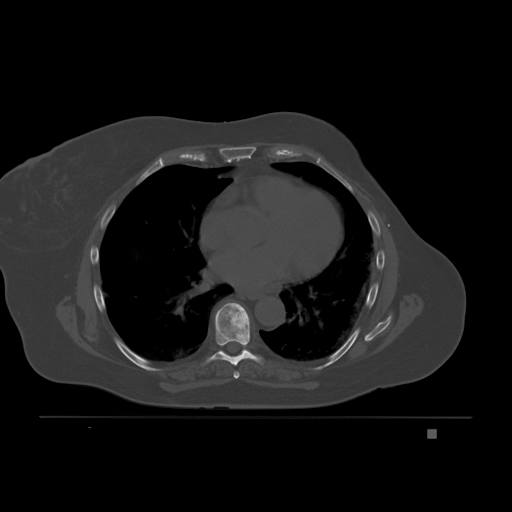
CT including the spine, one axial slice; slice 127 of 221 in the series (ordered by position); bone window (W 1800 / L 400 HU); 3 mm slice thickness; 512 × 512 image matrix, field of view 474 × 474 mm. Patient: female, 63 years. From the clinical record (not read from this slice): primary cancer: breast.
Outlined on this slice (semi-automatic segmentation, software-assisted and operator-edited):
- T6 vertebra: bounding box <234,371,240,379> (left, top, right, bottom; pixels)
- T7 vertebra: <206,302,263,366>